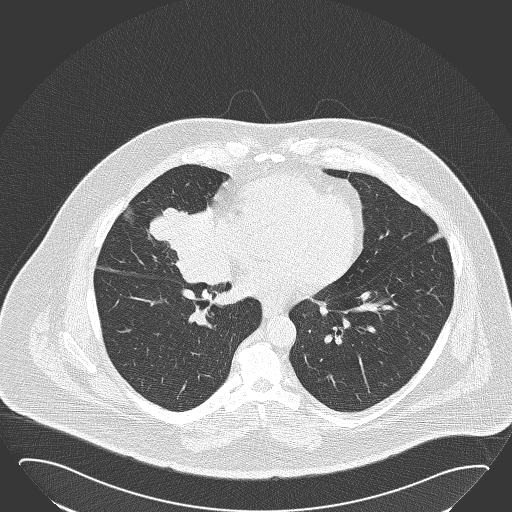
Low-dose screening chest CT, one axial slice; position 73 of 168 along the scan axis; reconstruction kernel B50f; 120 kVp; lung window (W 1500 / L -600 HU); 2 mm slice thickness; 512 × 512 image matrix, field of view 432 × 432 mm.
Outlined on this slice (manually delineated by an expert):
- lesion 1 (tumor, hilum of right lung): bounding box [x1, y1, x2, y2] px = [149, 205, 230, 286]